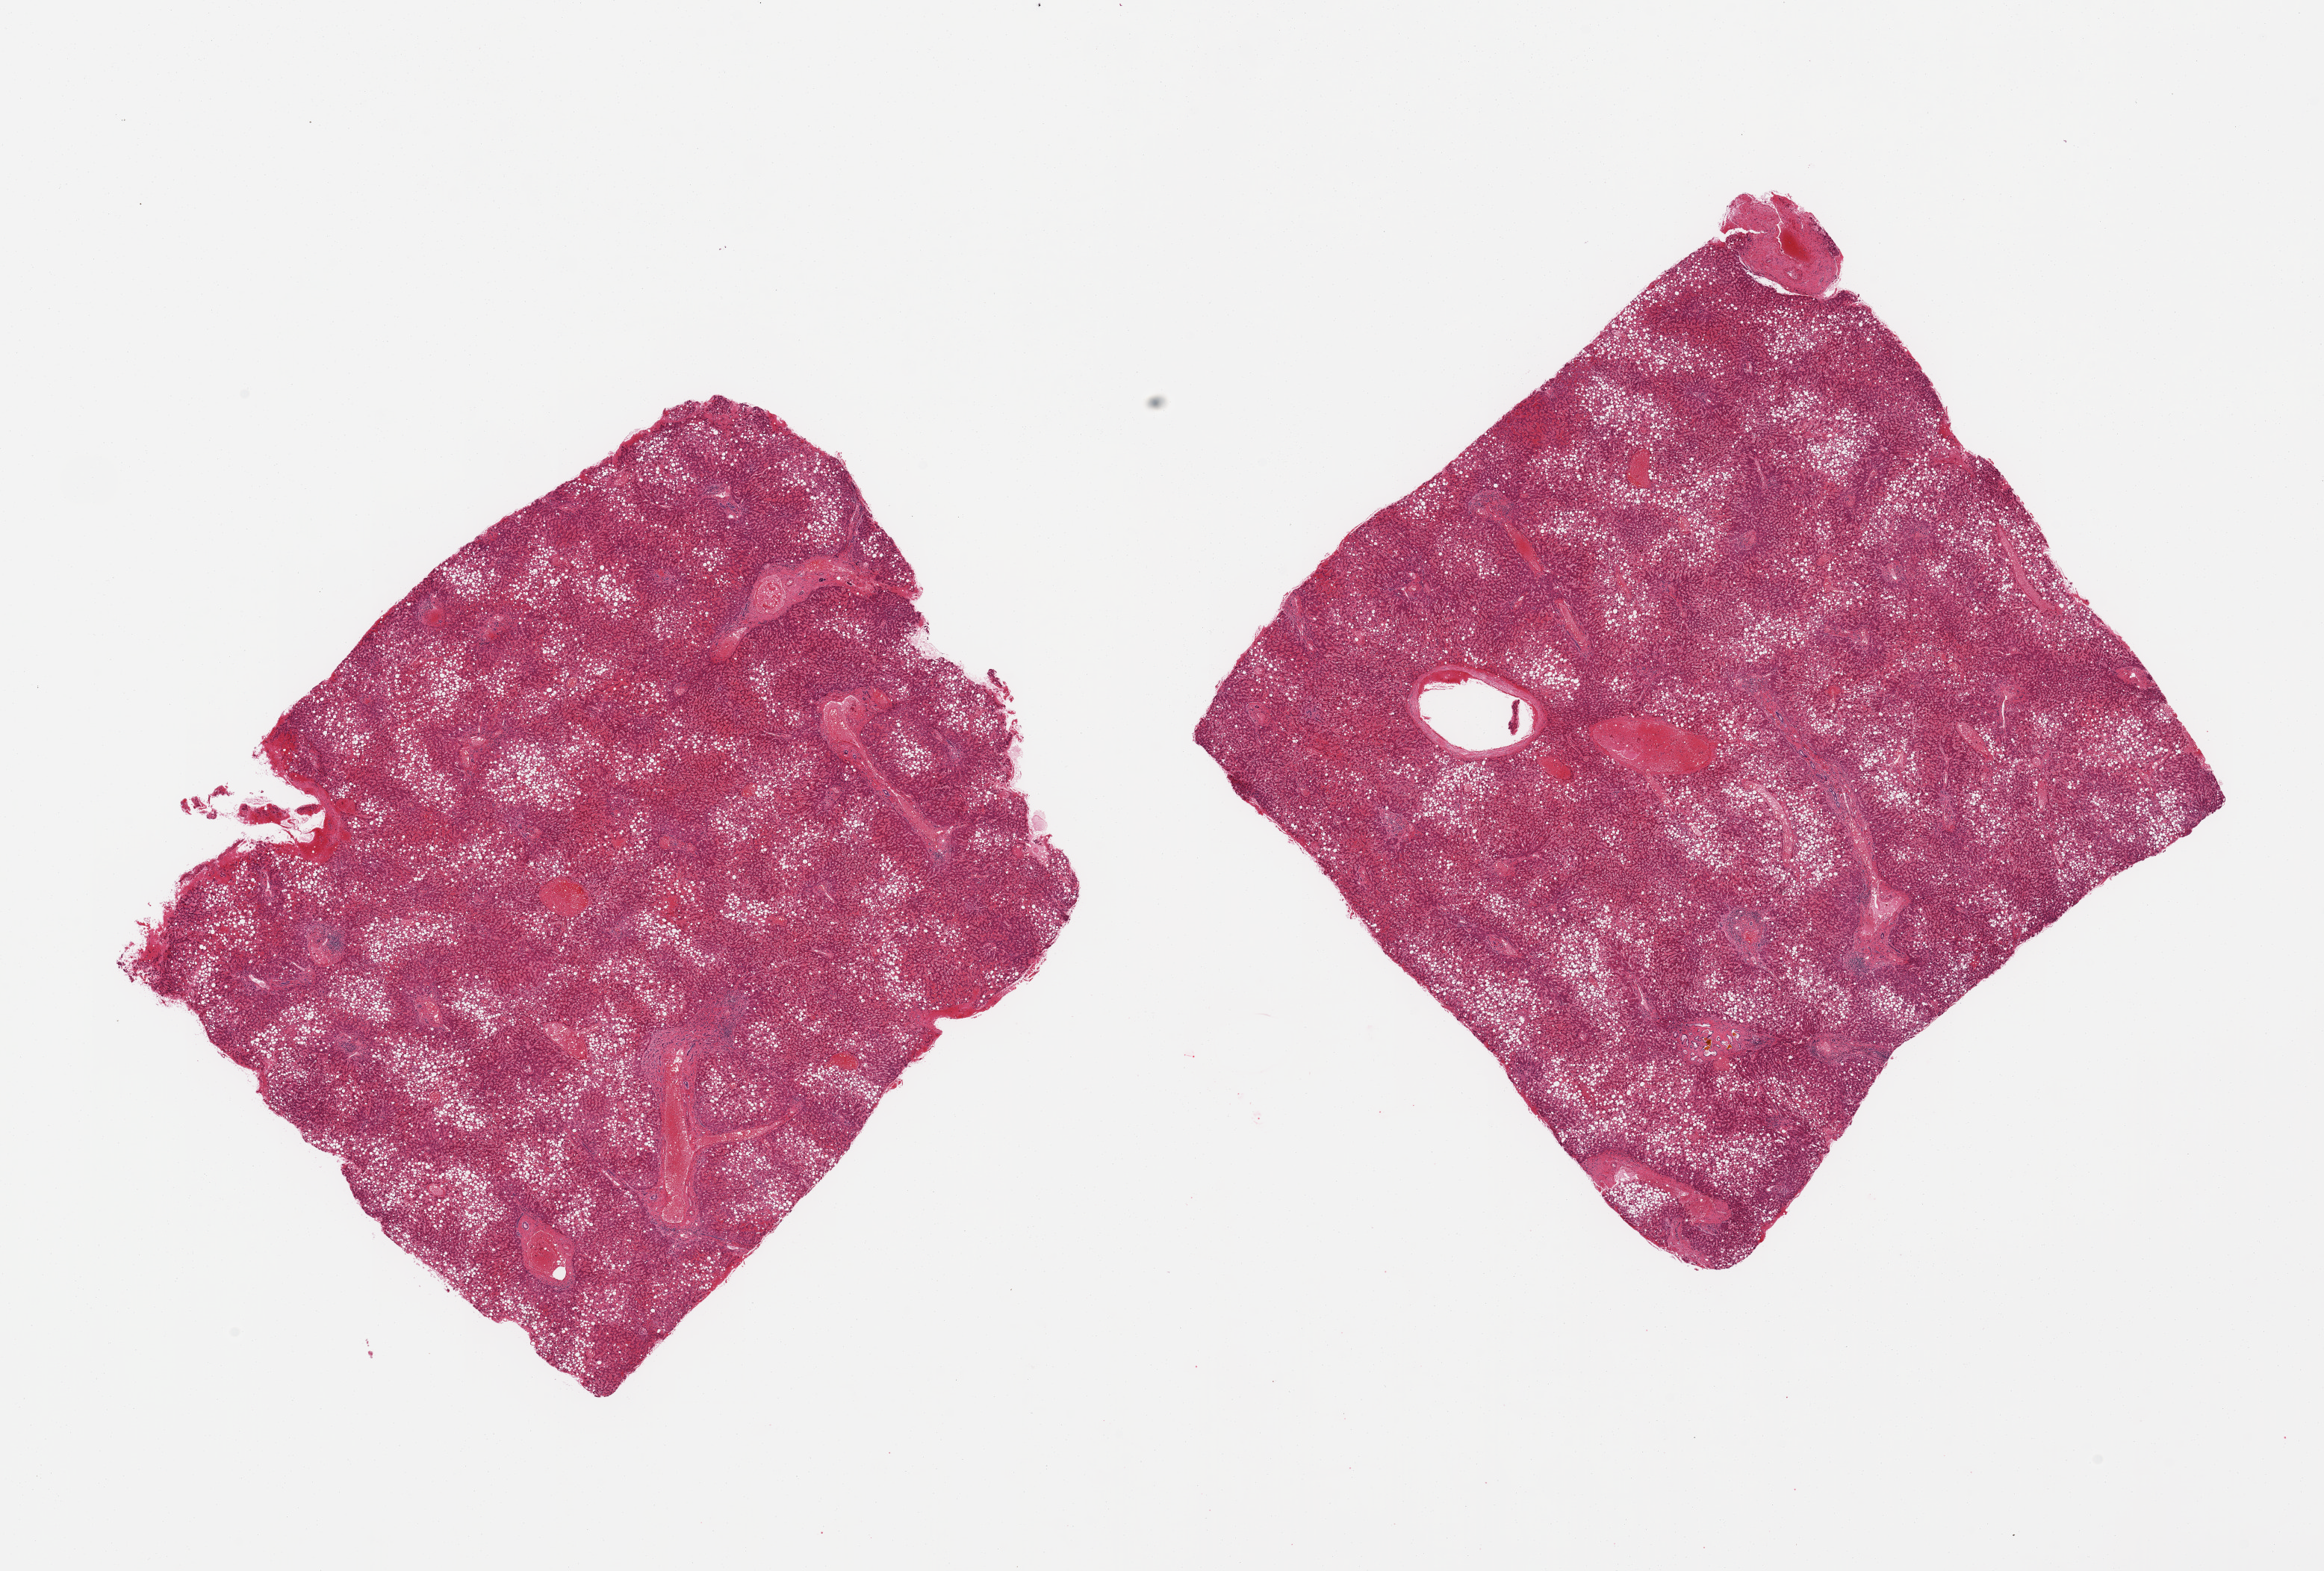
H&E whole-slide image — shown as a low-resolution overview of the whole scanned area (about 24.6 x 16.6 mm). PAXgene-fixed, paraffin-embedded tissue. Target tissue: liver. Tissue donor sample. Male donor.
Review note (as recorded): 2 pieces; severe centrilobular macrovesicular steatosis; 1 mm bile duct hamartoma (von Meyenberg complex).